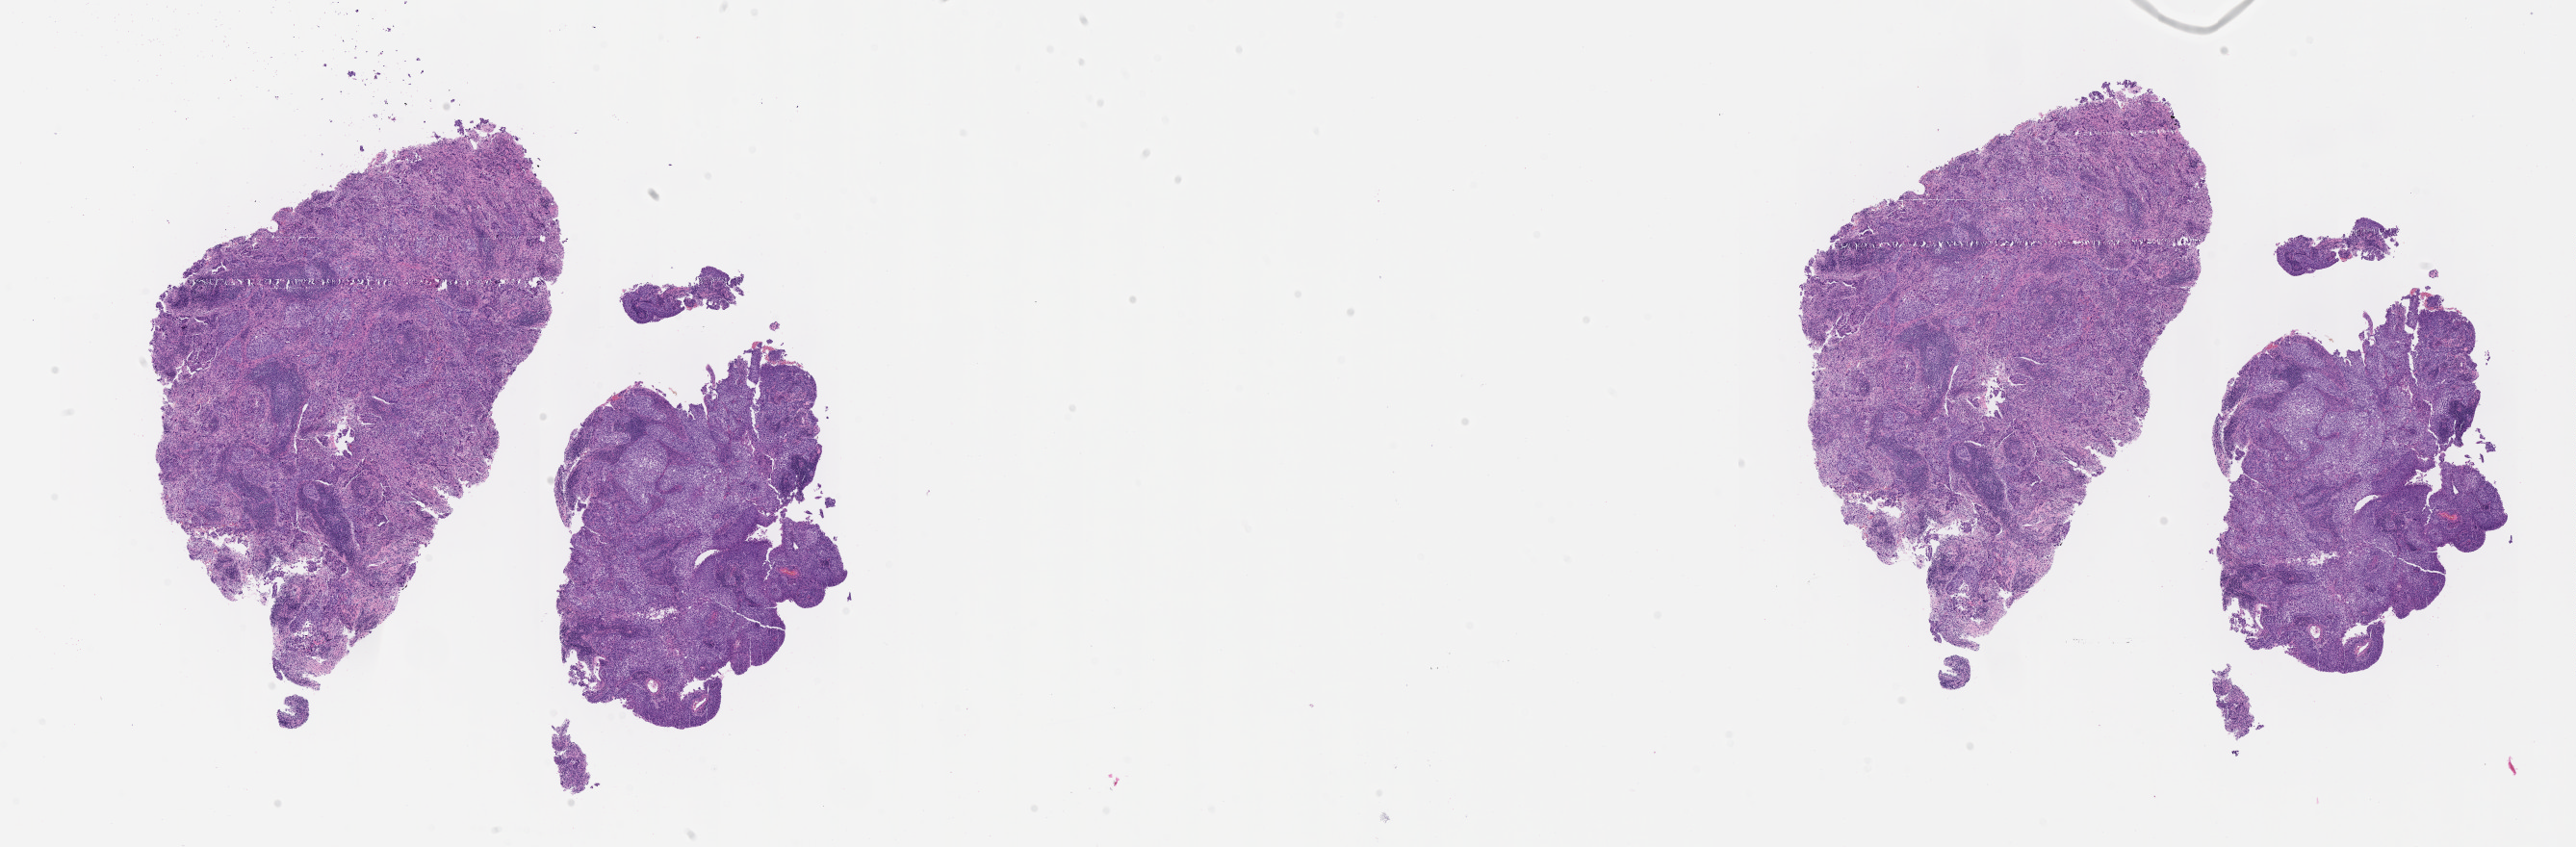
Whole-slide image, haematoxylin and eosin stain, low-resolution overview of the scanned area, about 21.6 x 7.1 mm; tumor tissue; site: cervix. Patient female; aged 74.
• histologic diagnosis: Squamous cell carcinoma, large cell, nonkeratinizing, NOS